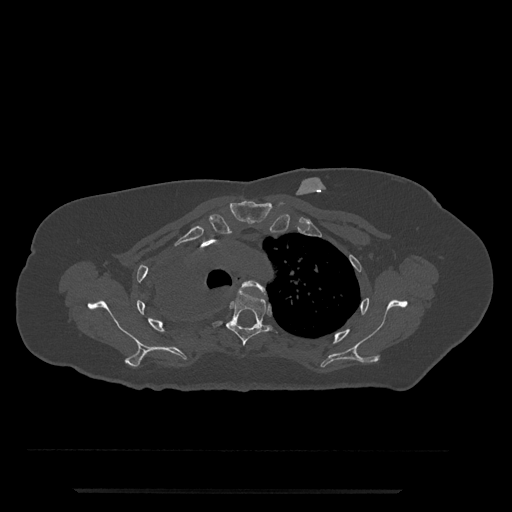
CT including the spine, one axial slice. Position 593 of 797 along the scan axis. Reconstruction kernel Br40s/3. 120 kVp. Bone window (W 1800 / L 400 HU). 0.5 mm slice thickness. 512 × 512 image matrix. Female patient, age 51 years. Case-level facts recorded for this patient, not image findings: primary cancer: neuro.
Outlined on this slice (semi-automatic segmentation, software-assisted and operator-edited):
- T3 vertebra: bounding box (x1, y1, x2, y2) in pixels: (242, 280, 265, 293)
- T4 vertebra: (214, 287, 278, 346)